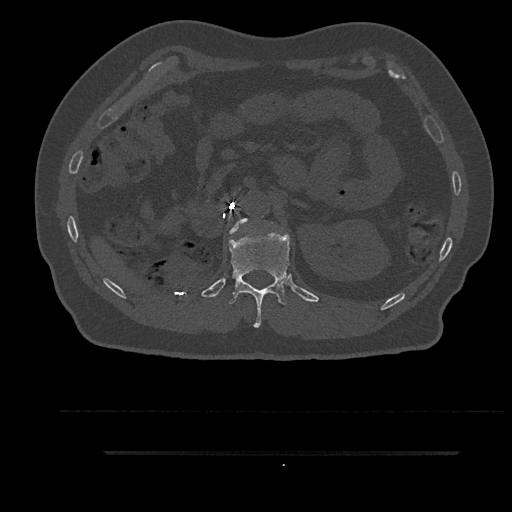
CT including the spine, one axial slice. Position 232 of 797 along the scan axis. Reconstruction kernel Br40s/3. 120 kVp. Bone window (W 1800 / L 400 HU). 0.5 mm slice thickness. 512 × 512 image matrix. Male patient, age 63 years. From the clinical record (not read from this slice): primary cancer: renal.
Structures marked on this image (semi-automatically segmented with operator editing):
- L1 vertebra: bounding box <230,219,248,234> (left, top, right, bottom; pixels)
- T12 vertebra: <228,231,290,328>